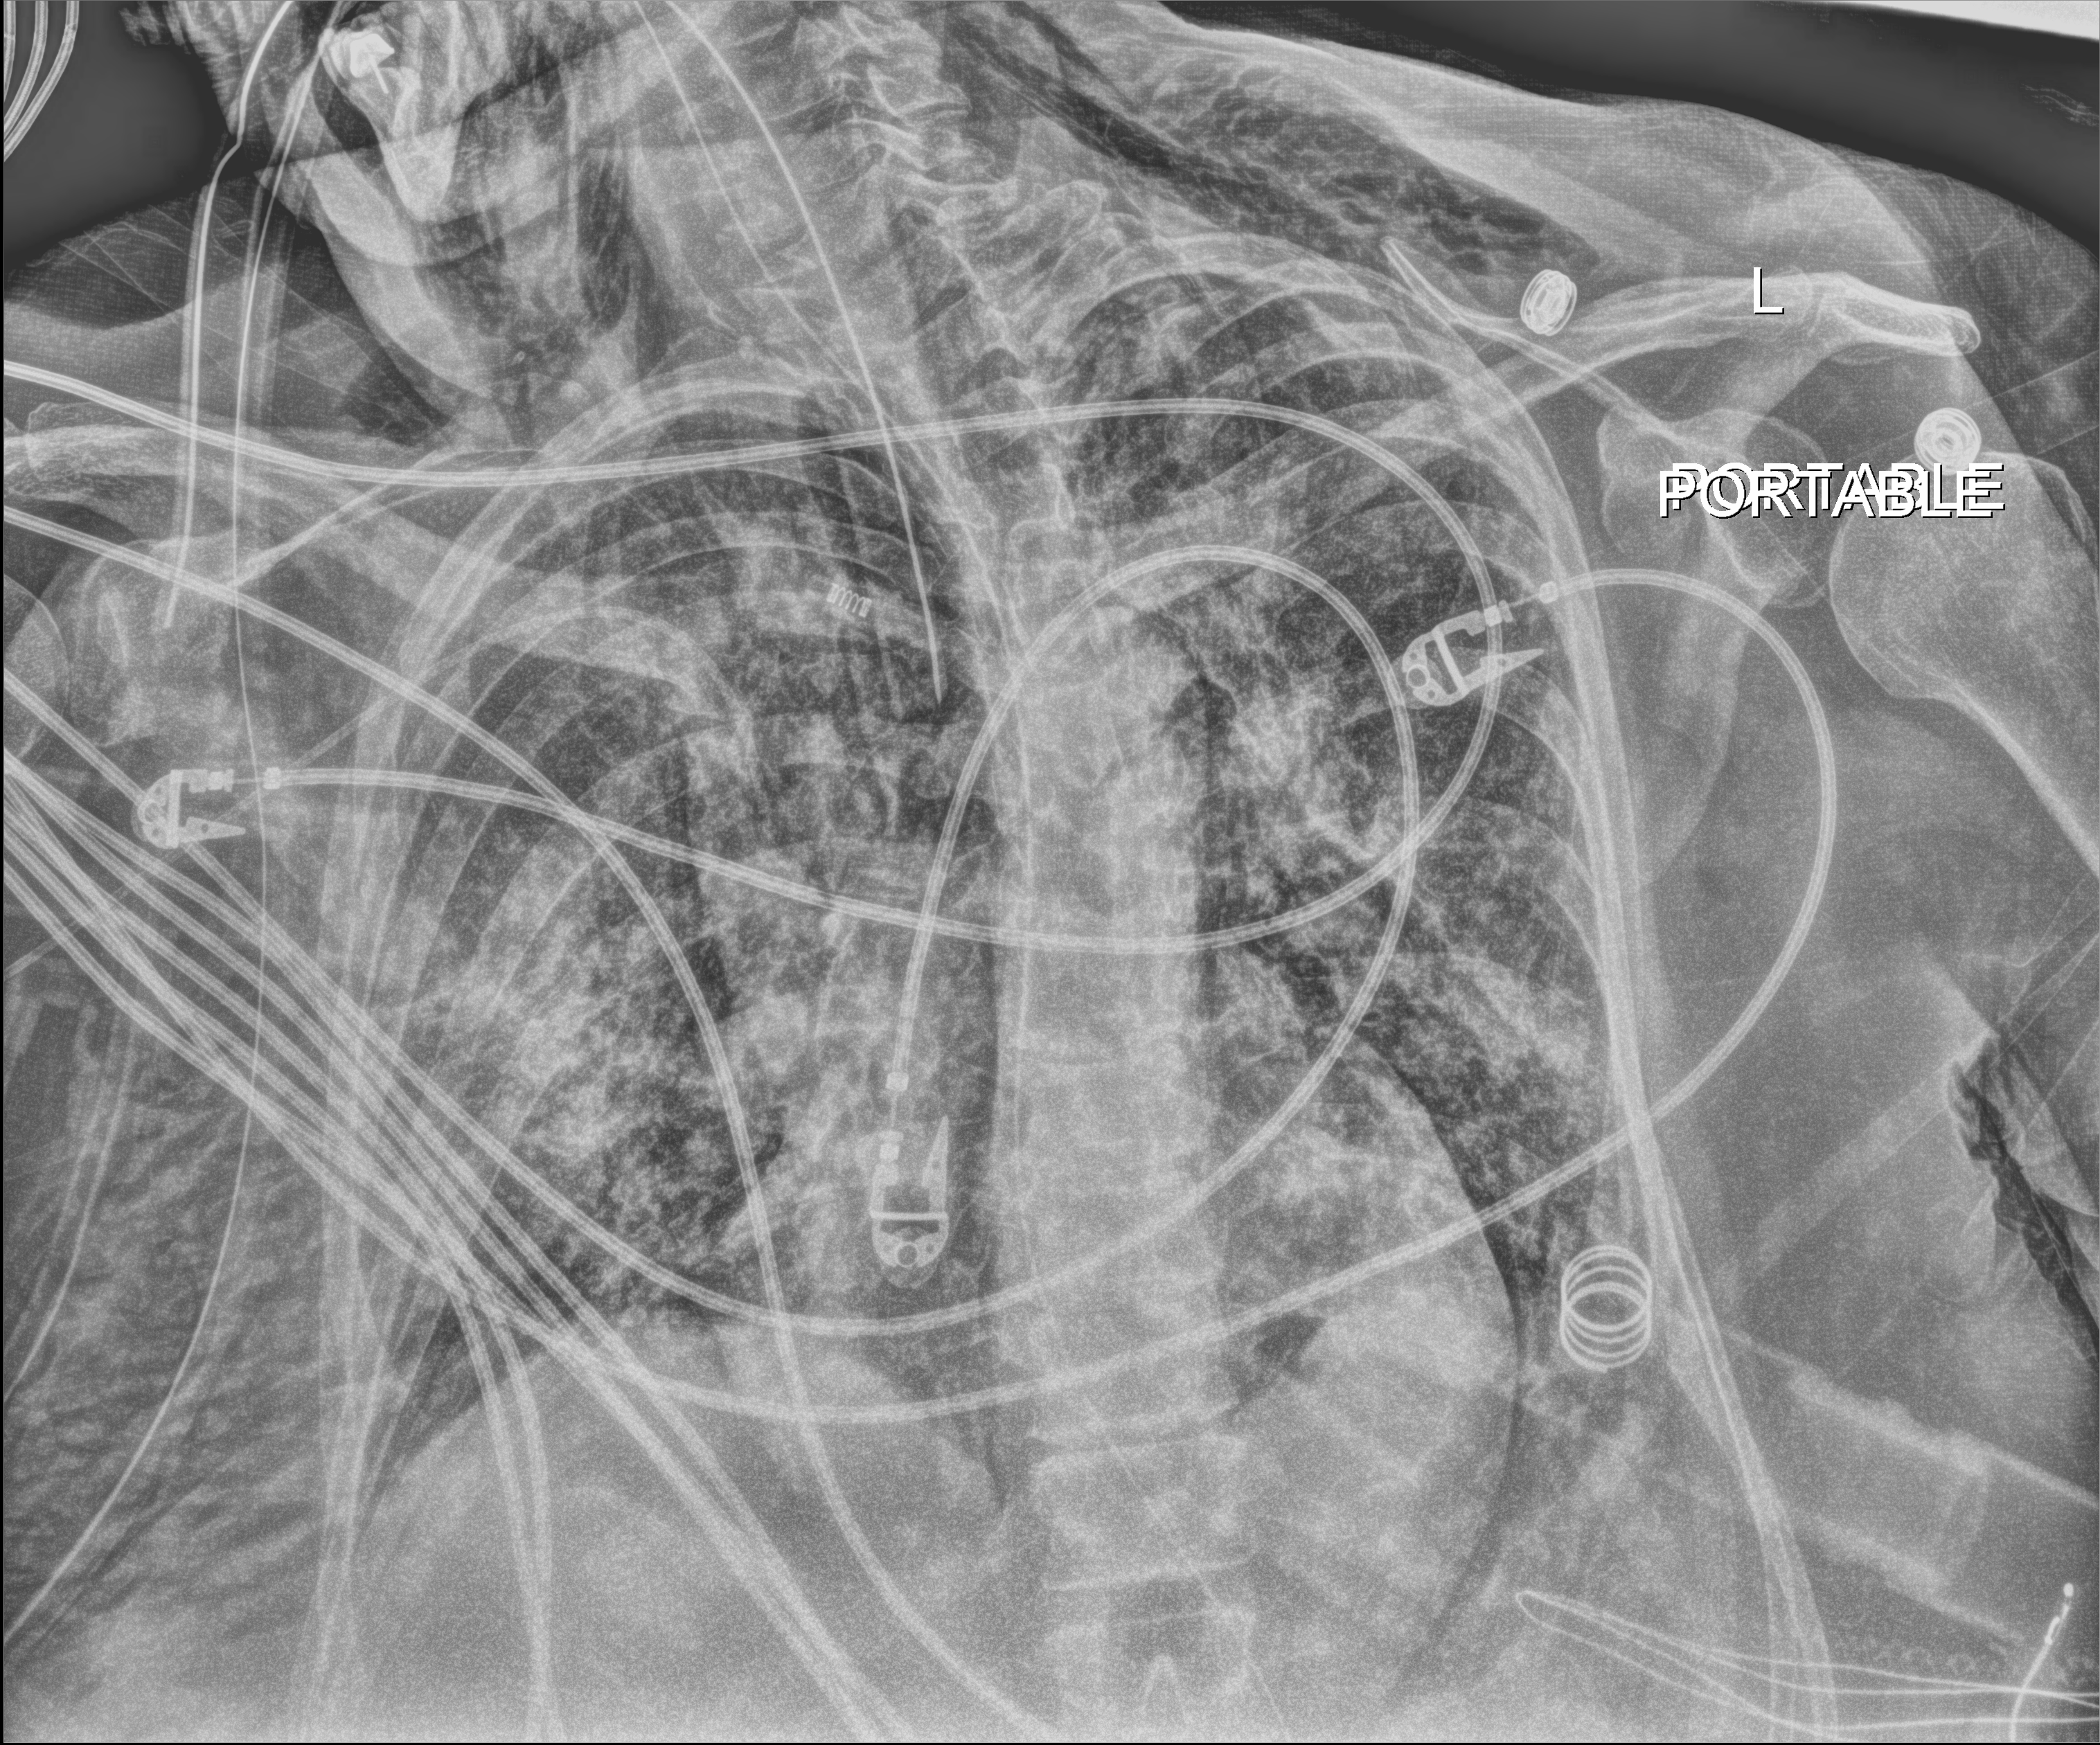
Bedside chest radiograph (digital radiography); anteroposterior (AP) projection. Female patient hospitalised with COVID-19, age 60–74 years.
From the hospital-stay record, not from the radiograph (when in the stay this image was taken is not recorded): mechanically ventilated during this hospital stay: yes; admitted to intensive care during this hospital stay: yes.